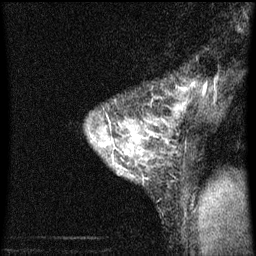
Breast MRI (dynamic contrast-enhanced), one sagittal slice; slice 50 of 60 in the series (ordered by position); dynamic contrast-enhanced series, image 2 of 3 at this slice position (ordered by acquisition); 1.5 T; TE 4.2 ms, TR 8 ms; 2 mm slice thickness; 256 × 256 image matrix, field of view 180 × 180 mm. Female patient, age 33 years.
Outlined on this slice (semi-automatically segmented with operator editing):
- analysis volume of interest (the breast-tissue region the enhancement analysis was run in; not a lesion): bounding box (x1, y1, x2, y2) in pixels: (86, 84, 199, 215)
- tumour enhancement mask (voxels above the 70 % enhancement threshold inside the analysis volume of interest): (99, 106, 179, 171)